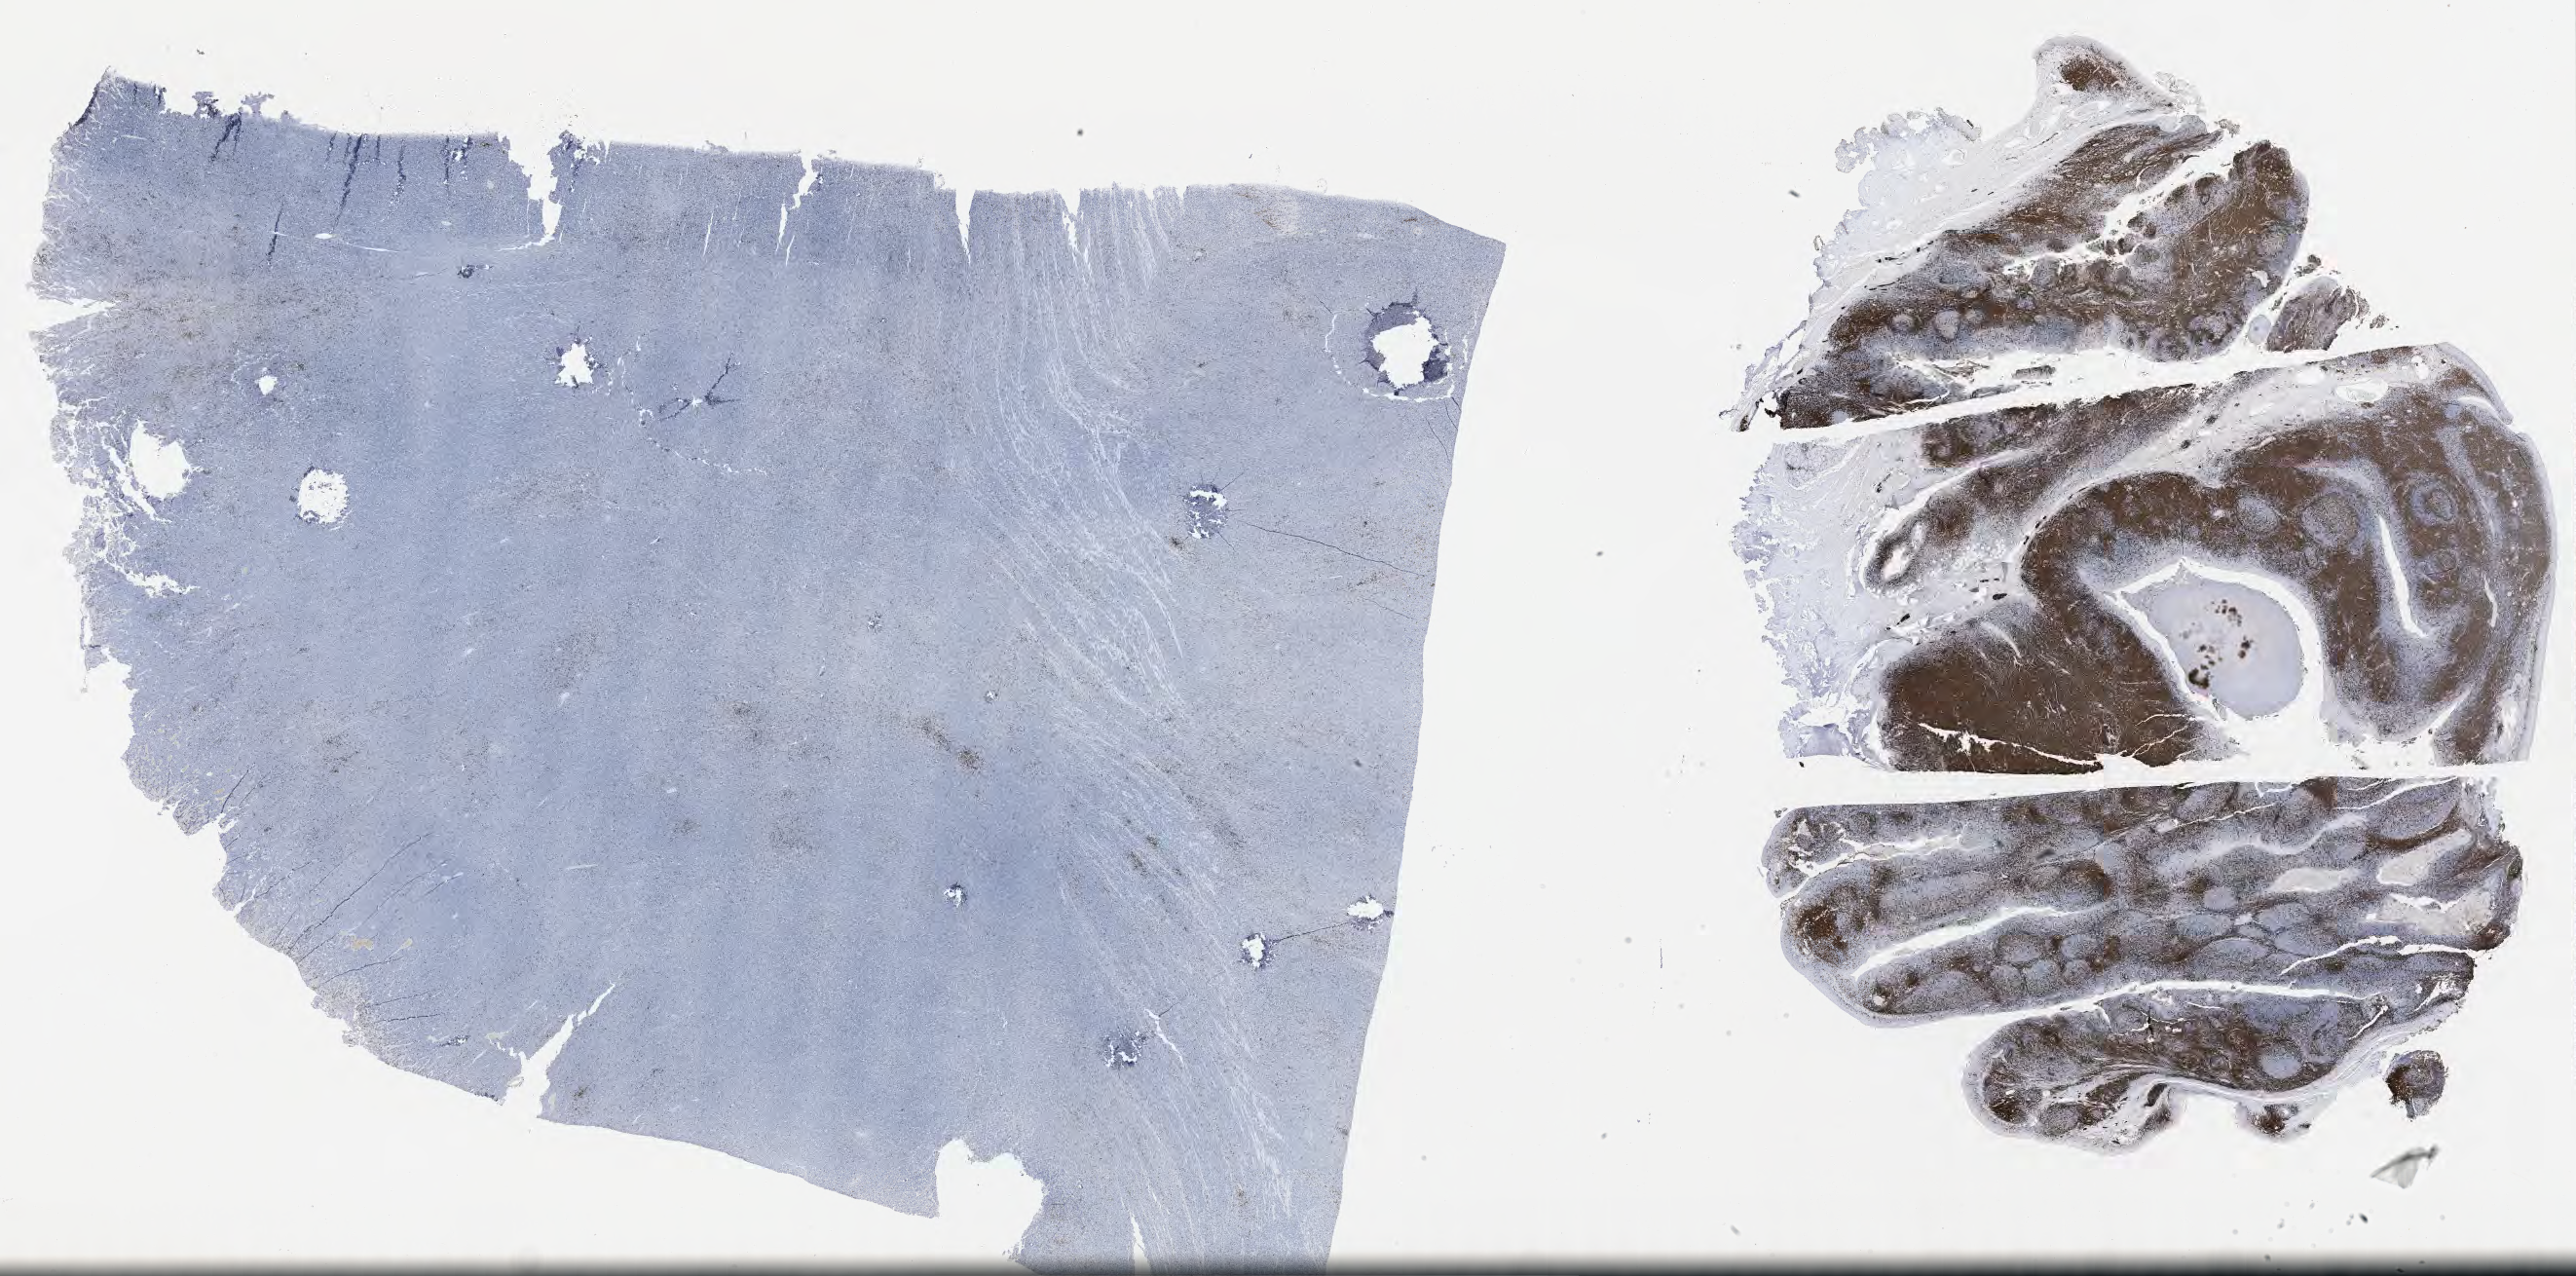
Immunohistochemistry (IHC) whole-slide image stained for CD3 — low-resolution overview of the scanned area, about 42.8 x 21.2 mm, specimen: tumor tissue. Patient male; aged 17.
* diagnosis: Burkitt lymphoma, NOS